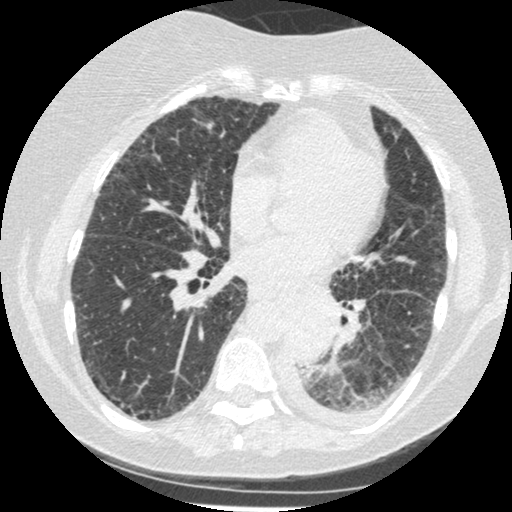
Low-dose screening chest CT, one axial slice. Slice 101 of 341 in the series (ordered by position). 120 kVp. Lung window (W 1500 / L -600 HU). 512 × 512 image matrix, field of view 310 × 310 mm.
Outlined on this slice (outlined manually by an expert reader):
- lesion 1 (tumor, lower lobe of left lung): box from (x=286, y=306) to (x=338, y=363) px